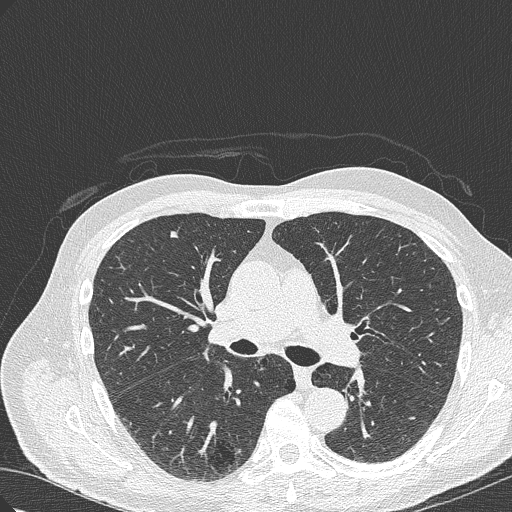
Low-dose screening chest CT, axial slice. First (baseline) screen. Lung window (W 1500 / L -600 HU). 120 kVp. Slice 127 of 322 in the series. 512 × 512 image matrix, field of view 350 × 350 mm. Male, age 70 years at enrolment. Current smoker at enrolment.
• Lesion marked by an expert reader, bounding box (x1, y1, x2, y2) in pixels: (200, 419, 264, 472).
• The screening reader recorded 4 non-calcified nodules or masses ≥4 mm on this exam; which of them this box marks is not recorded.
• Participant outcome: lung cancer diagnosed 978 days after this screen (after the third annual screen) — bronchiolo-alveolar adenocarcinoma, NOS, right lower lobe, poorly differentiated (G3), stage IB (AJCC 6th edition), 30 mm at pathology.